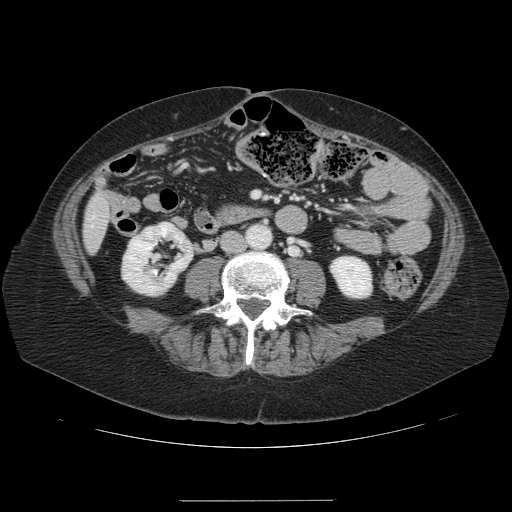
Contrast-enhanced abdominal CT, one axial slice; slice 15 of 141 in the series (ordered by position); 120 kVp; intravenous contrast given; soft-tissue window (W 400 / L 40 HU); 512 × 512 image matrix, field of view 393 × 393 mm. Female patient, age 74 years. From the clinical record (not read from this slice): diagnosis: colorectal cancer liver metastases, imaged before liver resection; multiple liver metastases: yes; largest metastasis: 7 cm; disease in both lobes: yes.
Structures marked on this image (outlined manually by an expert reader):
- liver: bounding box [x1, y1, x2, y2] px = [85, 195, 110, 252]
- planned liver remnant (the part of the liver to remain after resection): [88, 223, 110, 252]